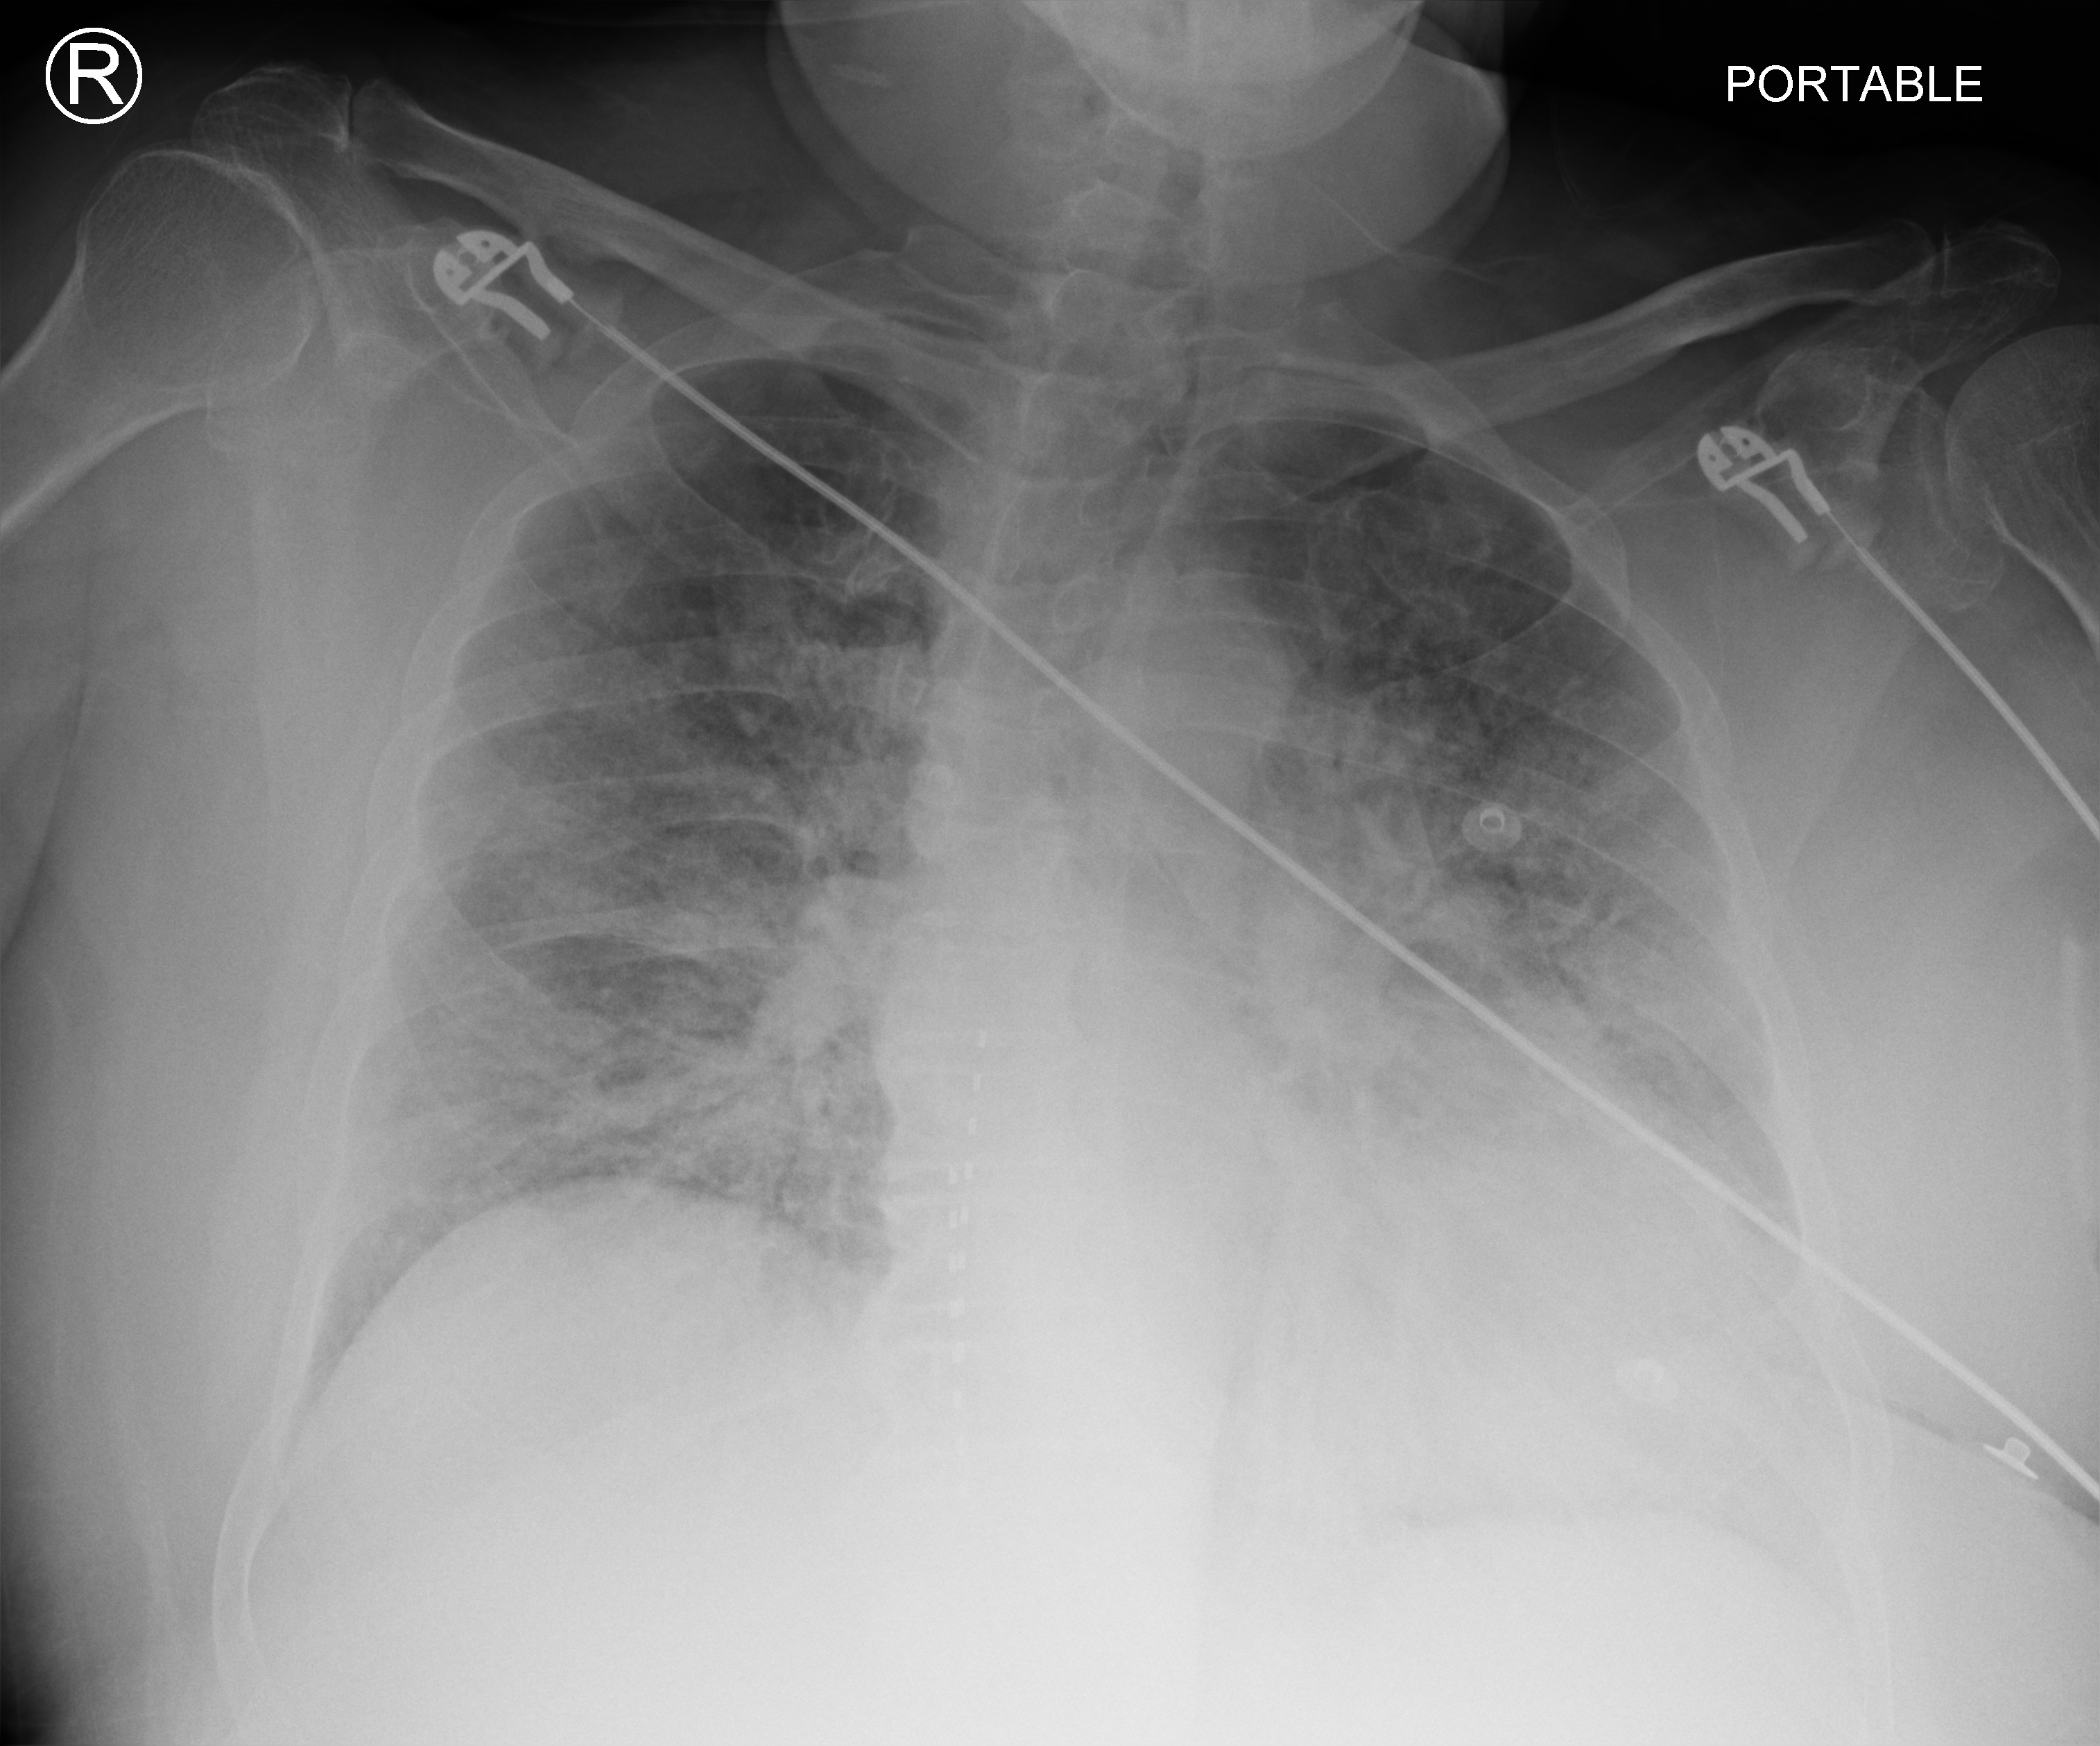
Bedside chest radiograph (computed radiography); anteroposterior (AP) projection. Patient hospitalised with COVID-19; male, aged 60–74 years.
Hospital-stay facts (about this admission, not read from this image; timing relative to this image not recorded):
- admitted to intensive care during this hospital stay: no
- COPD (admission record): no